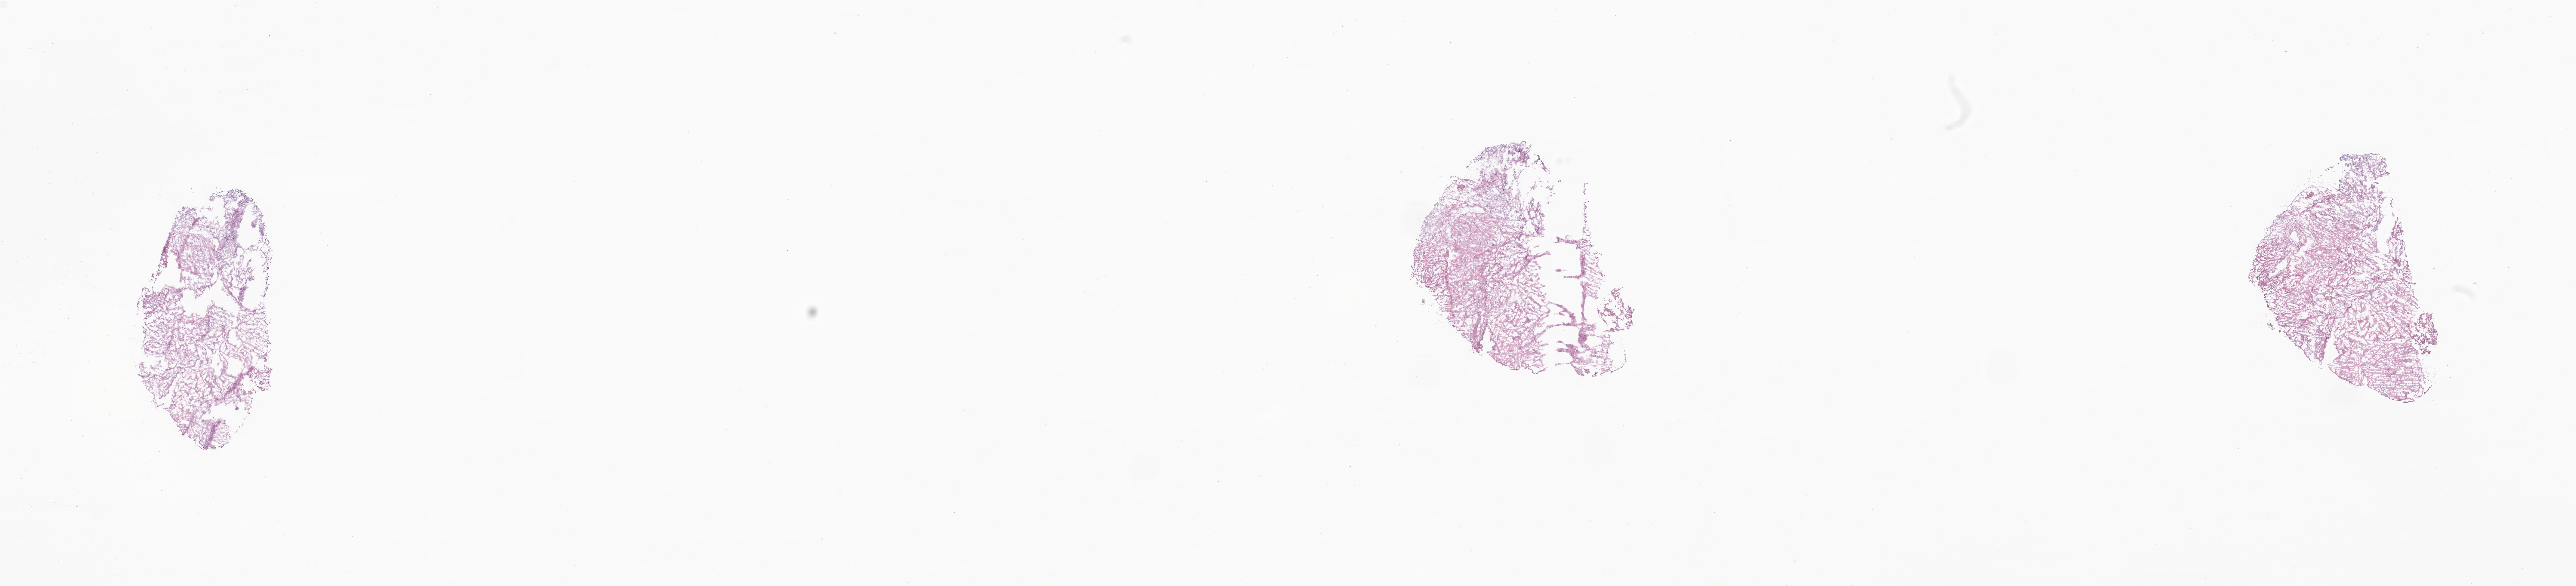
Digitized H&E-stained section of tumor tissue from the brain — shown as a low-resolution overview of the whole scanned area (about 36.1 x 8.2 mm), frozen section. Patient male; age 976 days (about 2.7 years).
Diagnosis (ICD-O-3 morphology term): Pilocytic astrocytoma.